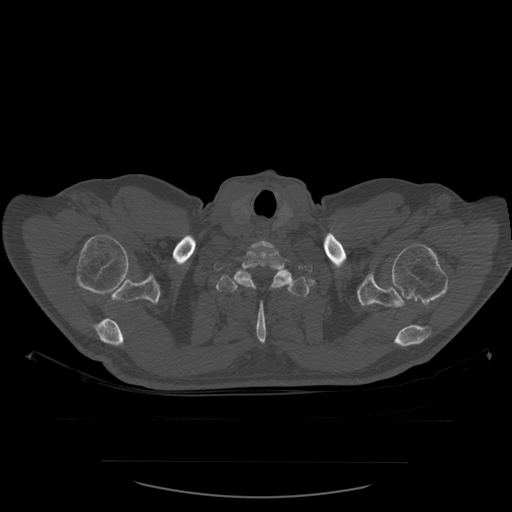
CT including the spine, one axial slice; position 484 of 590 along the scan axis; bone window (W 1800 / L 400 HU); 512 × 512 image matrix, field of view 479 × 479 mm. Patient age 71 years. Case-level facts recorded for this patient, not image findings: primary cancer: lung; vertebrae with lytic lesions (as recorded): T1, T2, L5, S1.
Structures marked on this image (semi-automatically segmented with operator editing):
- T1 vertebra: bounding box (x1, y1, x2, y2) in pixels: (214, 246, 313, 289)
- T2 vertebra: (216, 267, 317, 344)